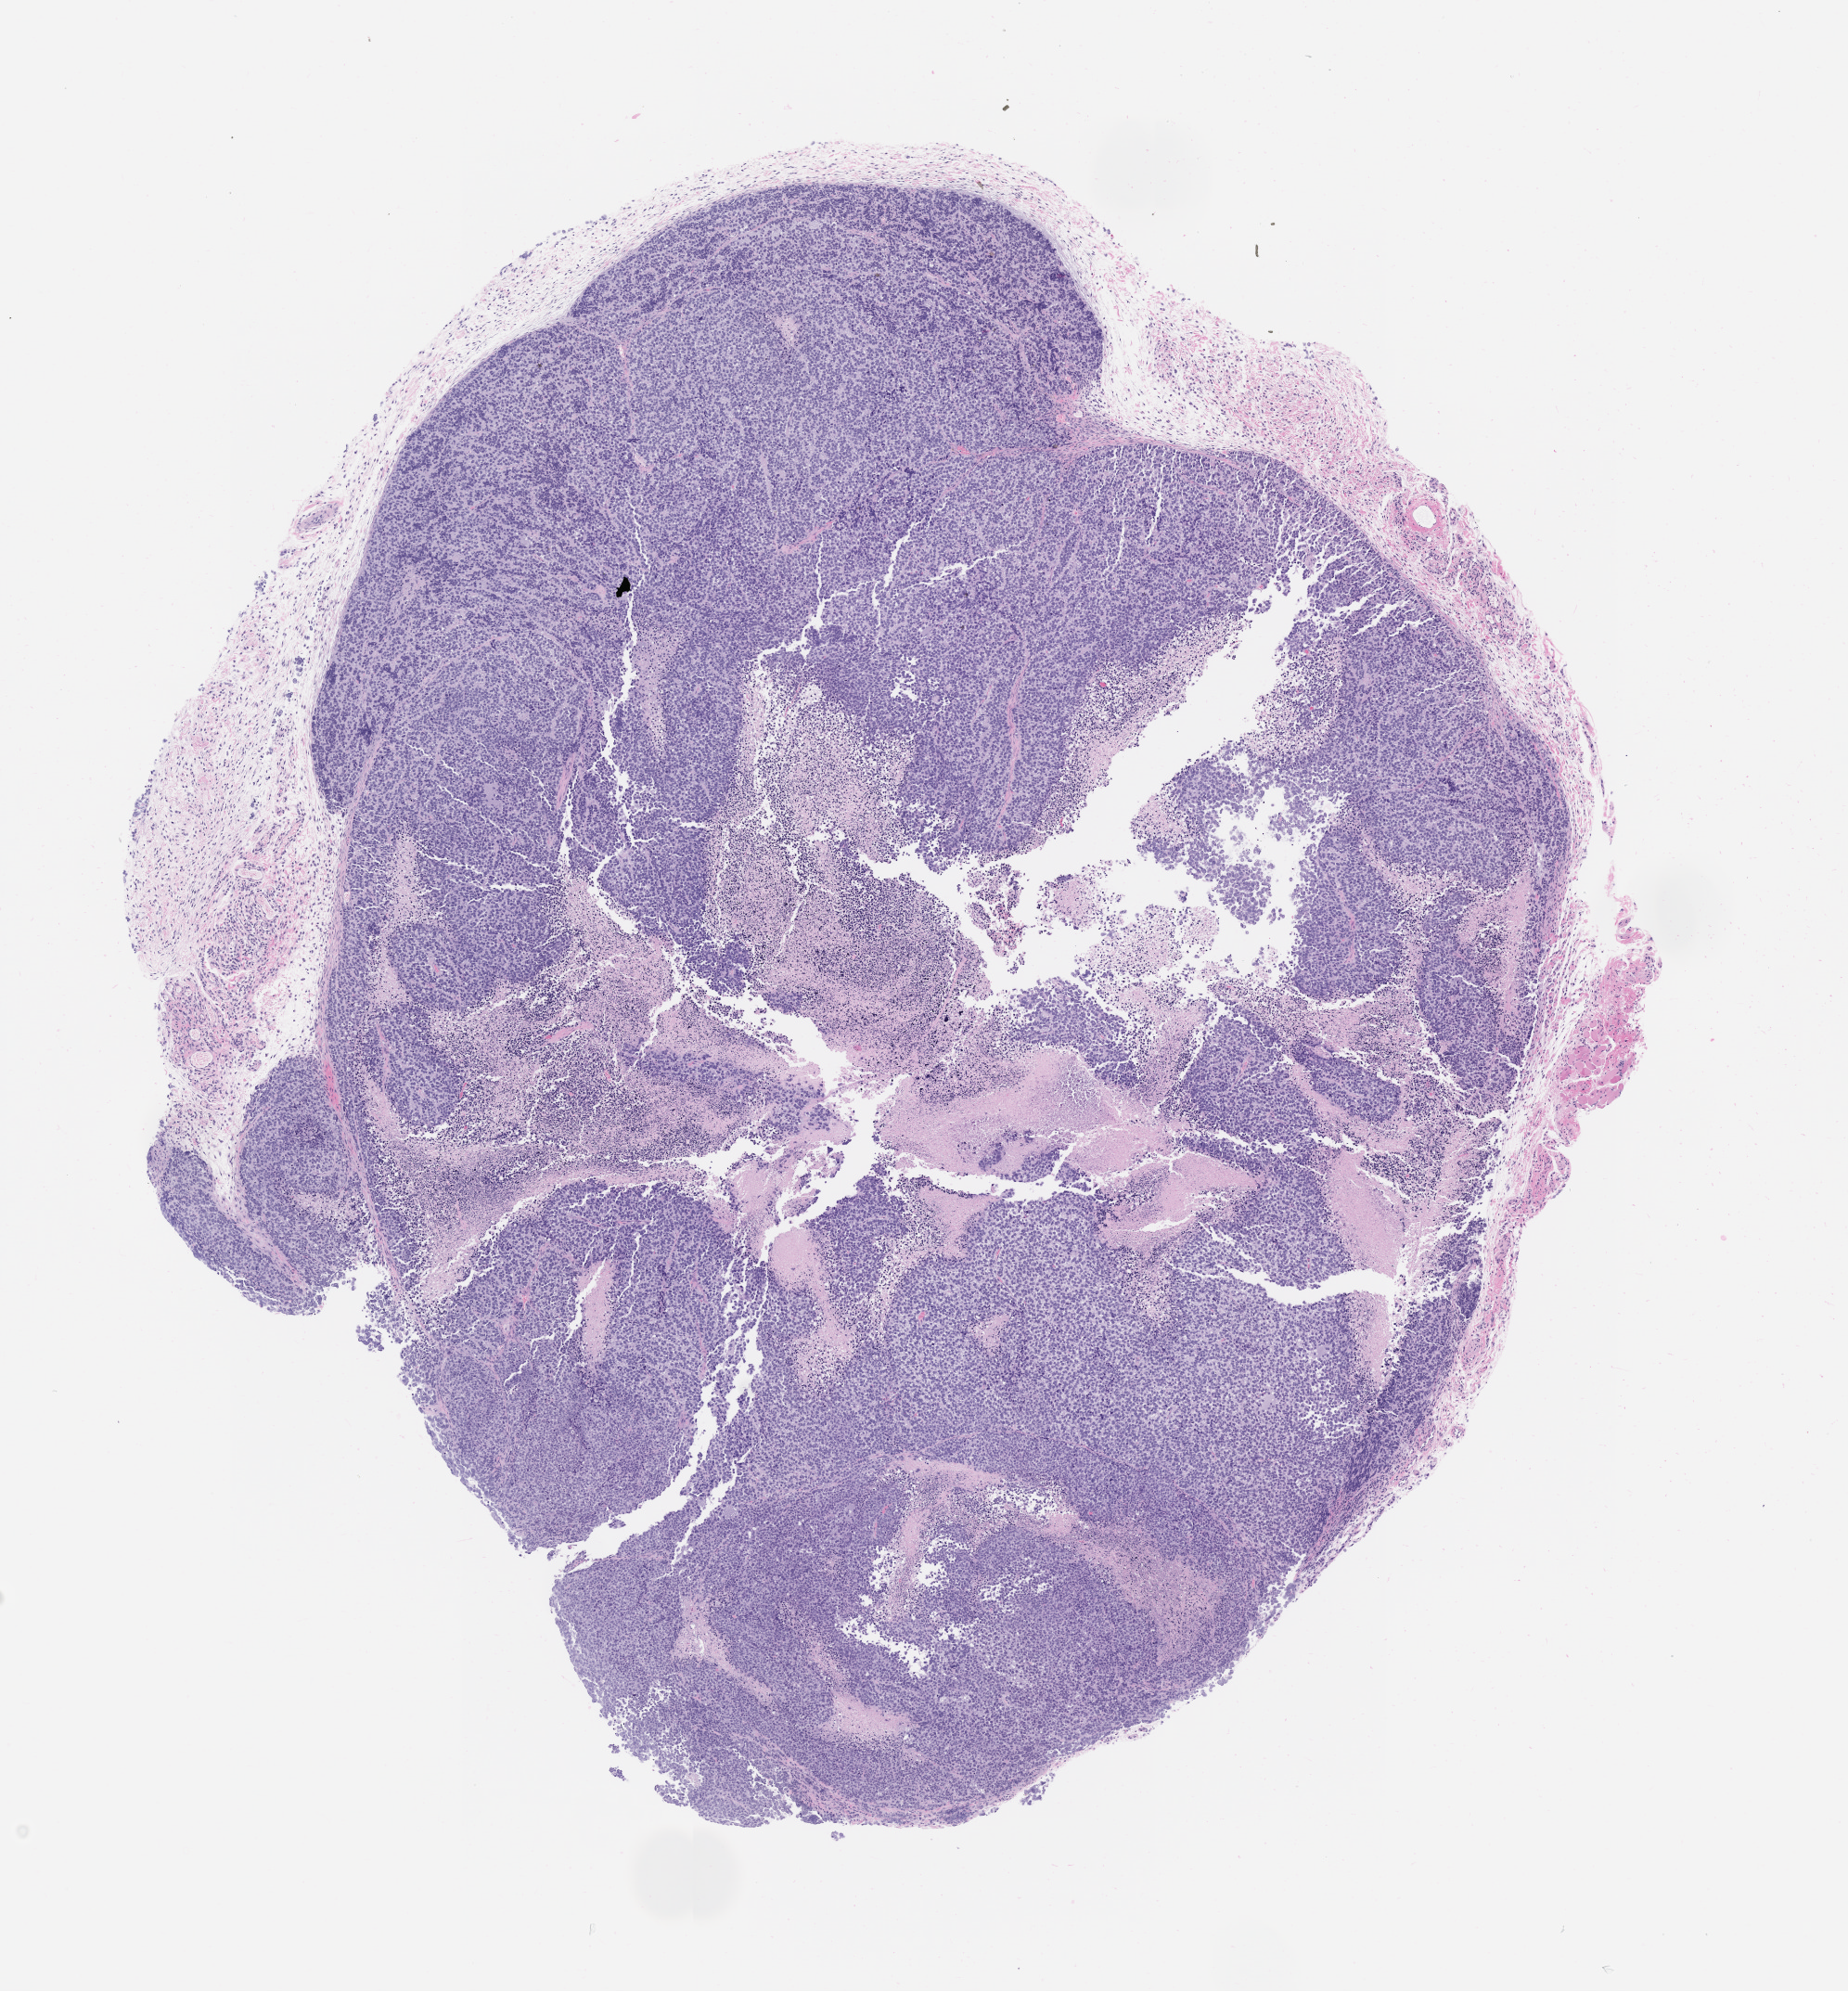
H&E whole-slide image of a patient-derived xenograft (PDX) tumor grown in a mouse, passage 1 — low-resolution overview of the scanned area, about 8.0 x 8.6 mm; formalin-fixed paraffin-embedded section; tumor site category: musculoskeletal.
Originating patient diagnosis: Ewing Sarcoma|Primitive Neuroectodermal Tumor.